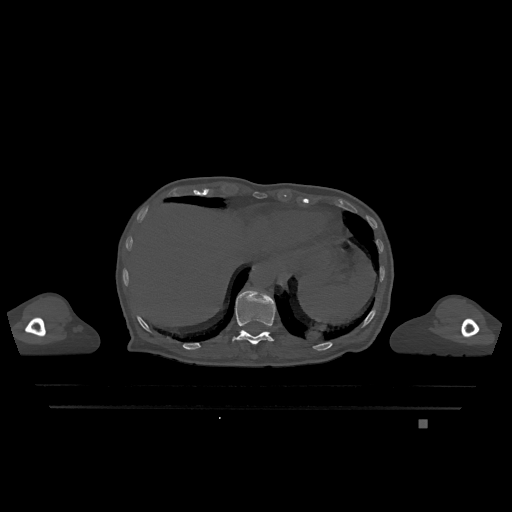
CT including the spine, one axial slice. Position 586 of 1317 along the scan axis. Bone window (W 1800 / L 400 HU). 0.5 mm slice thickness. 512 × 512 image matrix, field of view 500 × 500 mm. Female patient, age 74 years. Case-level facts recorded for this patient, not image findings: primary cancer: lung; vertebrae with lytic lesions (as recorded): T1, T4, T5, T6, L4, L5.
Annotated regions visible in this slice (semi-automatic segmentation, software-assisted and operator-edited):
- T11 vertebra: box from (x=232, y=289) to (x=276, y=345) px